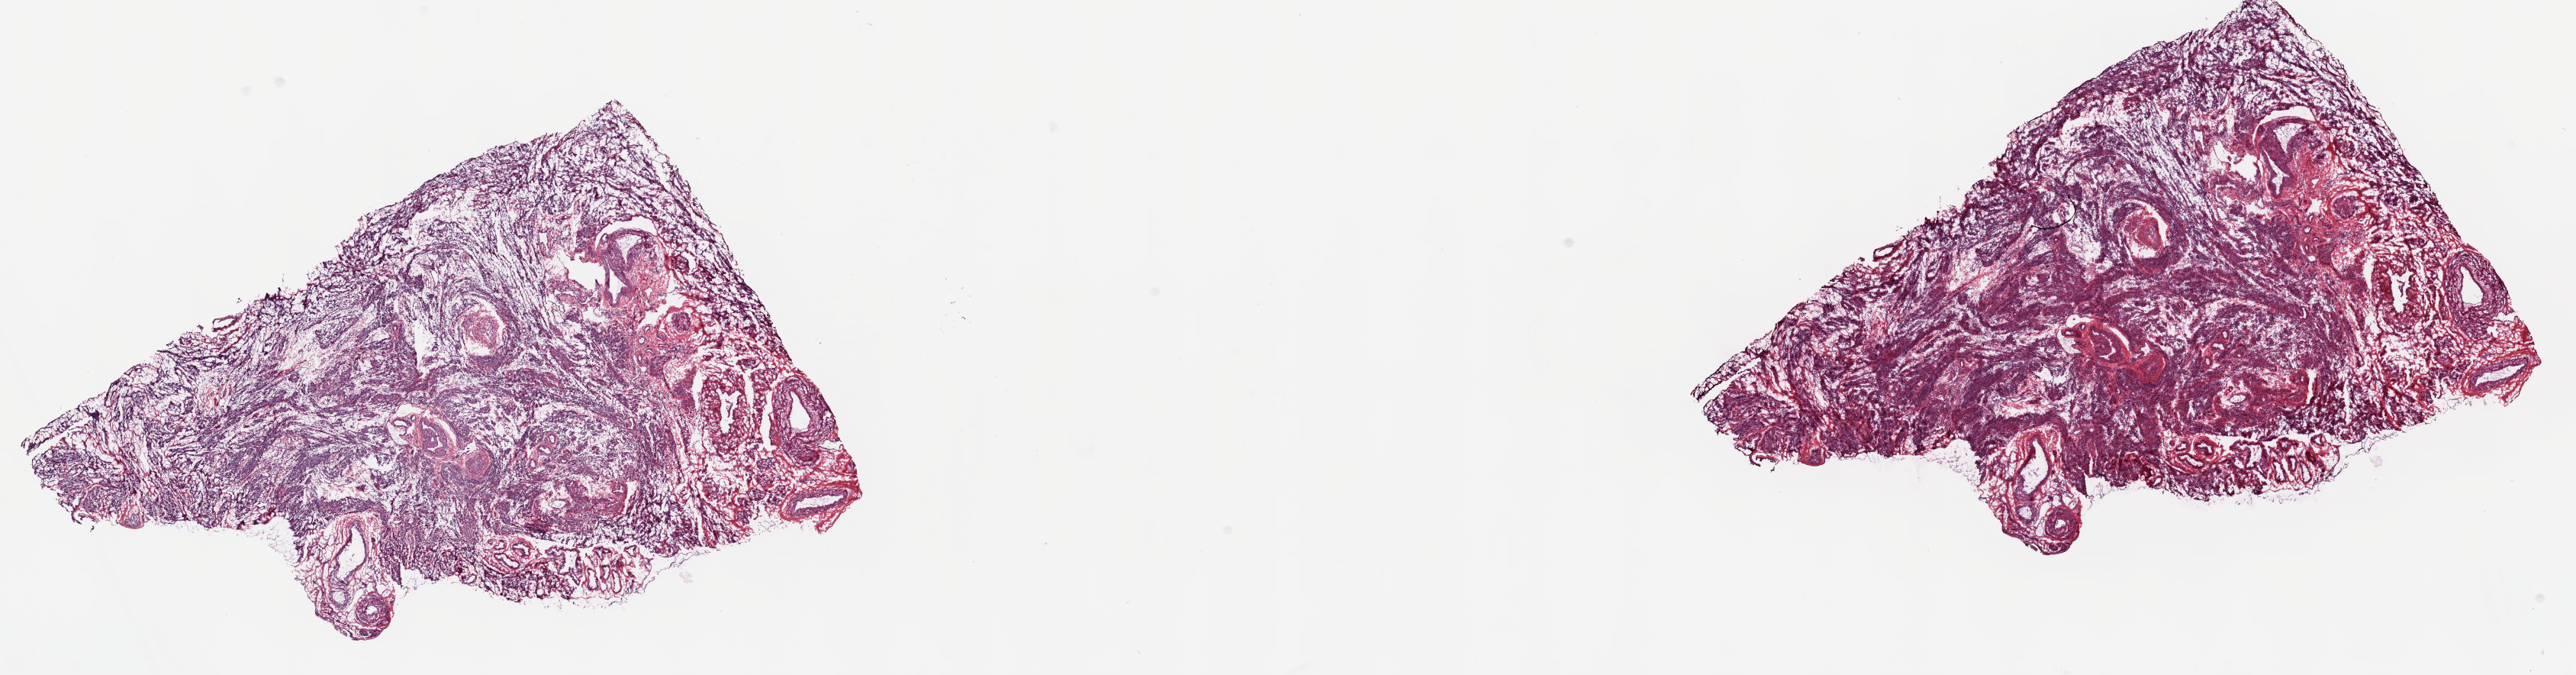
Whole-slide histology image, H&E-stained, whole scanned area (about 26.8 x 7.0 mm) shown as a low-resolution overview; frozen section from the top of the tissue portion; uterus, solid tissue normal (non-tumour tissue) sample. Patient: female, age at initial diagnosis 71 years. Composition of this section per pathologist review: tumour cells 0%, tumour nuclei 0%, normal cells 100%, stromal cells 0%, necrosis 0%. Inflammatory infiltration, as recorded: lymphocyte infiltration 1%, monocyte infiltration 0%, neutrophil infiltration 0%.
- this section: solid tissue normal (non-tumour) sample from the same patient
- patient diagnosis: Leiomyosarcoma, NOS